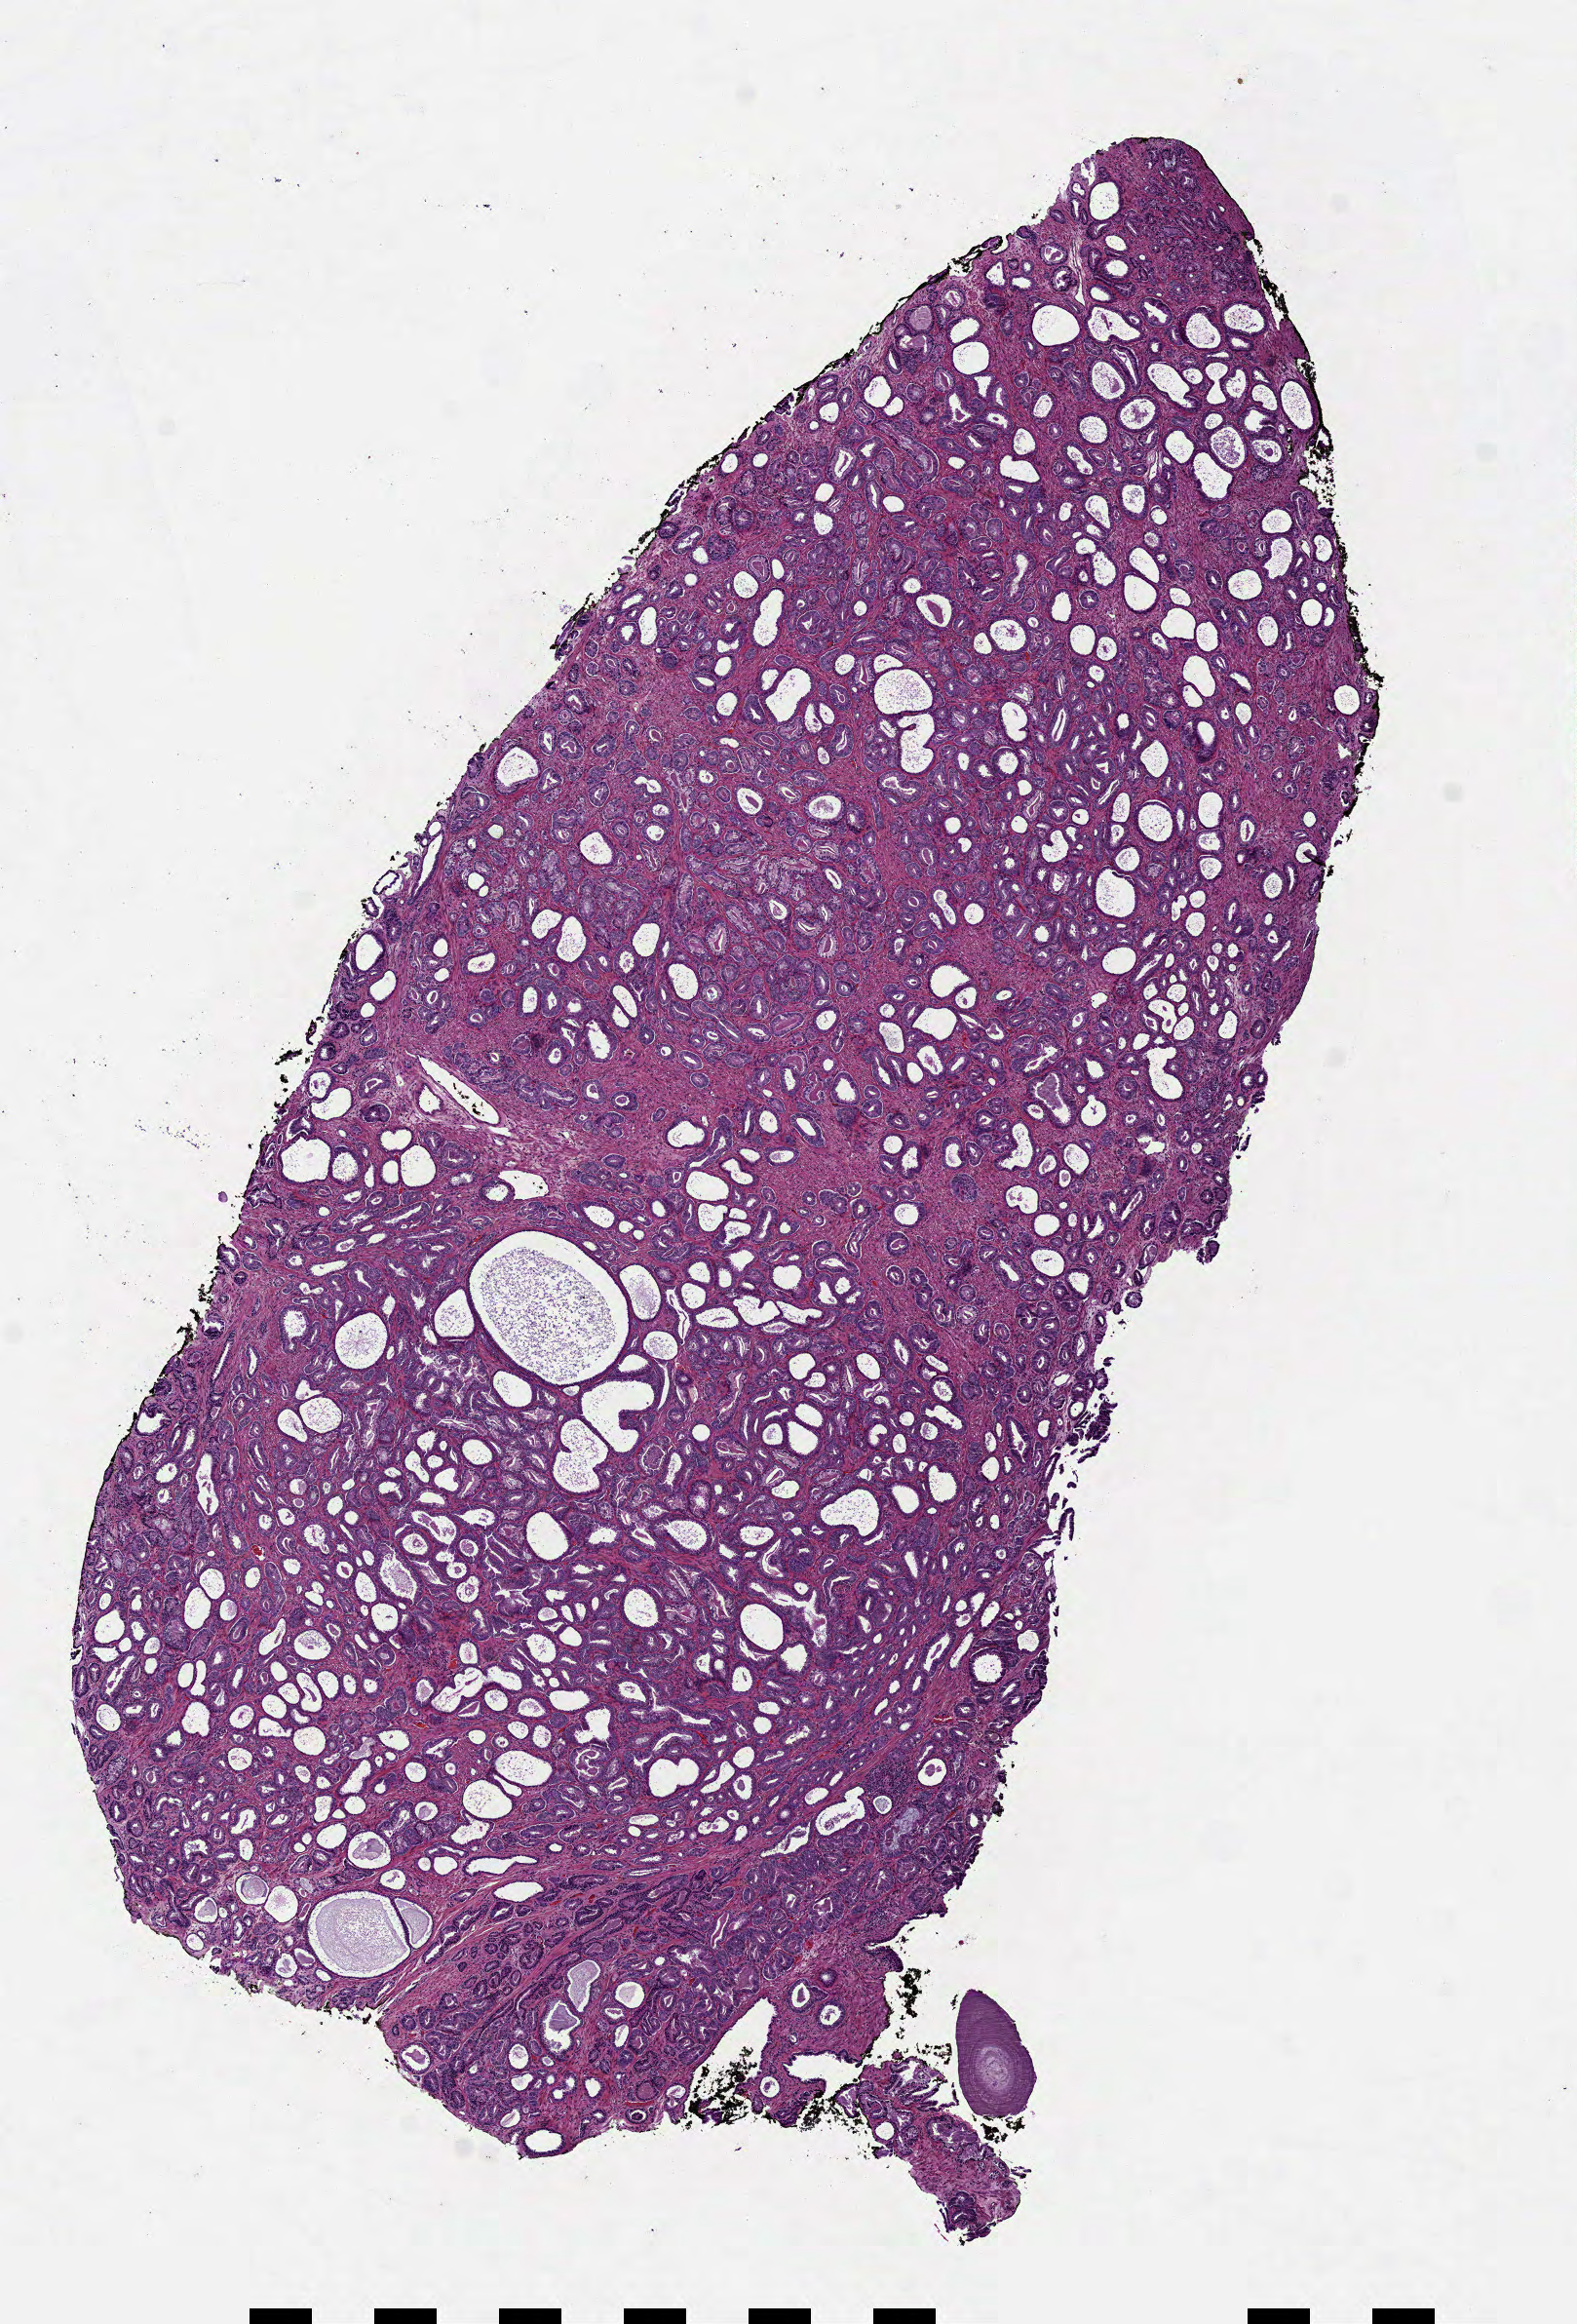
Digitized H&E-stained tissue section (whole slide), low-resolution overview of the scanned area, about 6.5 x 9.6 mm. FFPE section. Primary tumour sample from the prostate. Male, age 62 years at initial diagnosis.
Diagnosis: Adenocarcinoma, NOS (prostate gland).